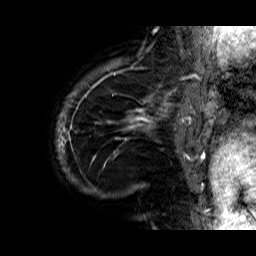
Breast MRI (dynamic contrast-enhanced), one sagittal slice. Slice 4 of 60 in the series (ordered by position). Dynamic contrast-enhanced series, time point 2 of 6 at this slice position (early post-contrast). 1.5 T. TE 6.3 ms, TR 32.9 ms. 4 mm slice thickness. 256 × 256 image matrix. Female patient. Case-level facts recorded for this patient, not image findings: setting: breast cancer imaged before/during neoadjuvant chemotherapy; receptor status: HR-positive, HER2-negative.
Outlined on this slice (semi-automatic segmentation, software-assisted and operator-edited):
- analysis volume of interest (the breast-tissue region the enhancement analysis was run in; not a lesion): bounding box [x1, y1, x2, y2] px = [56, 74, 176, 206]
- tumour enhancement mask (voxels above the 100 % enhancement threshold inside the analysis volume of interest): [56, 79, 154, 197]